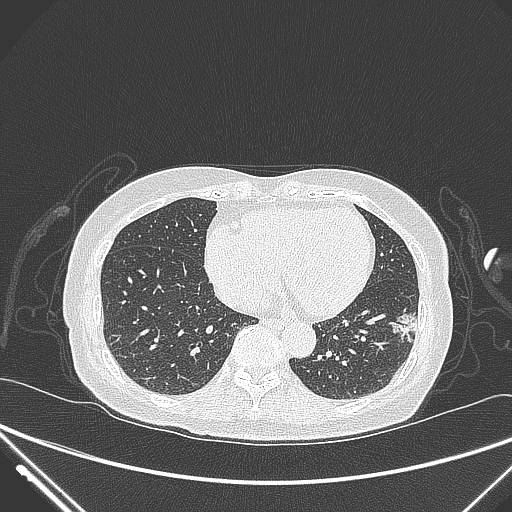
Chest CT, one axial slice. Slice 106 of 310 in the series (ordered by position). 120 kVp. Lung window (W 1500 / L -600 HU). 512 × 512 image matrix, field of view 377 × 377 mm. Female patient, age 82 years. Case-level facts recorded for this patient, not image findings: clinical TNM (as recorded): T1c N0 M0.
Annotated regions visible in this slice (bounding box drawn by a radiologist):
- lung tumour (recorded histology: adenocarcinoma): bounding box (x1, y1, x2, y2) in pixels: (389, 304, 428, 351)